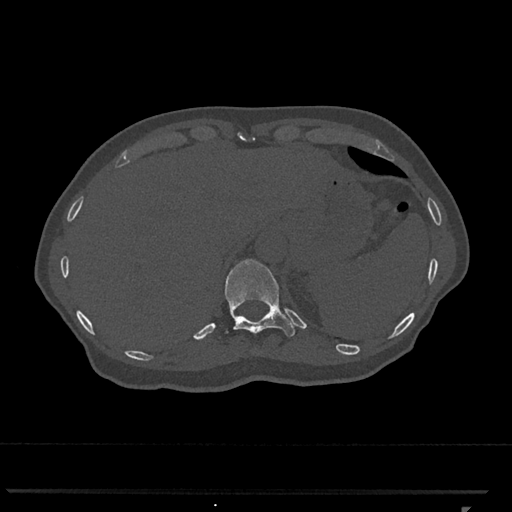
CT including the spine, one axial slice. Slice 519 of 793 in the series (ordered by position). 120 kVp. Bone window (W 1800 / L 400 HU). 512 × 512 image matrix. Female patient, age 62 years. Case-level facts recorded for this patient, not image findings: primary cancer: renal.
Outlined on this slice (semi-automatic segmentation, software-assisted and operator-edited):
- T11 vertebra: bounding box [x1, y1, x2, y2] px = [225, 259, 295, 338]